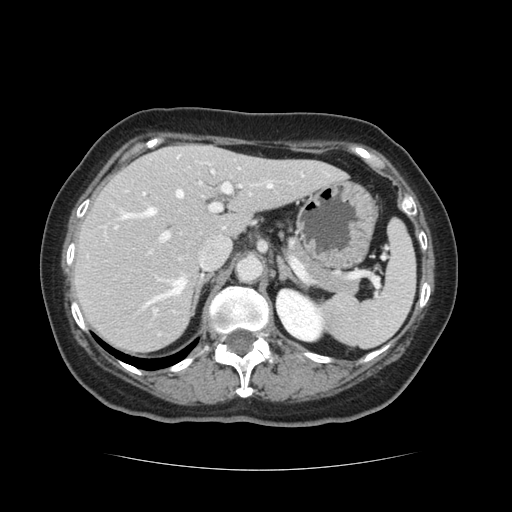
Contrast-enhanced abdominal CT, one axial slice. Position 81 of 128 along the scan axis. Intravenous contrast given. Soft-tissue window (W 400 / L 40 HU). 2.5 mm slice thickness. 512 × 512 image matrix. Female patient, age 67 years. Case-level facts recorded for this patient, not image findings: diagnosis: colorectal cancer liver metastases, imaged before liver resection; multiple liver metastases: yes; largest metastasis: 3 cm; chemotherapy before resection: no.
Outlined on this slice (manually delineated by an expert):
- hepatic veins: bounding box [x1, y1, x2, y2] px = [123, 184, 272, 304]
- liver: [74, 145, 342, 353]
- planned liver remnant (the part of the liver to remain after resection): [74, 157, 342, 353]
- portal vein (with intrahepatic branches): [114, 160, 266, 243]